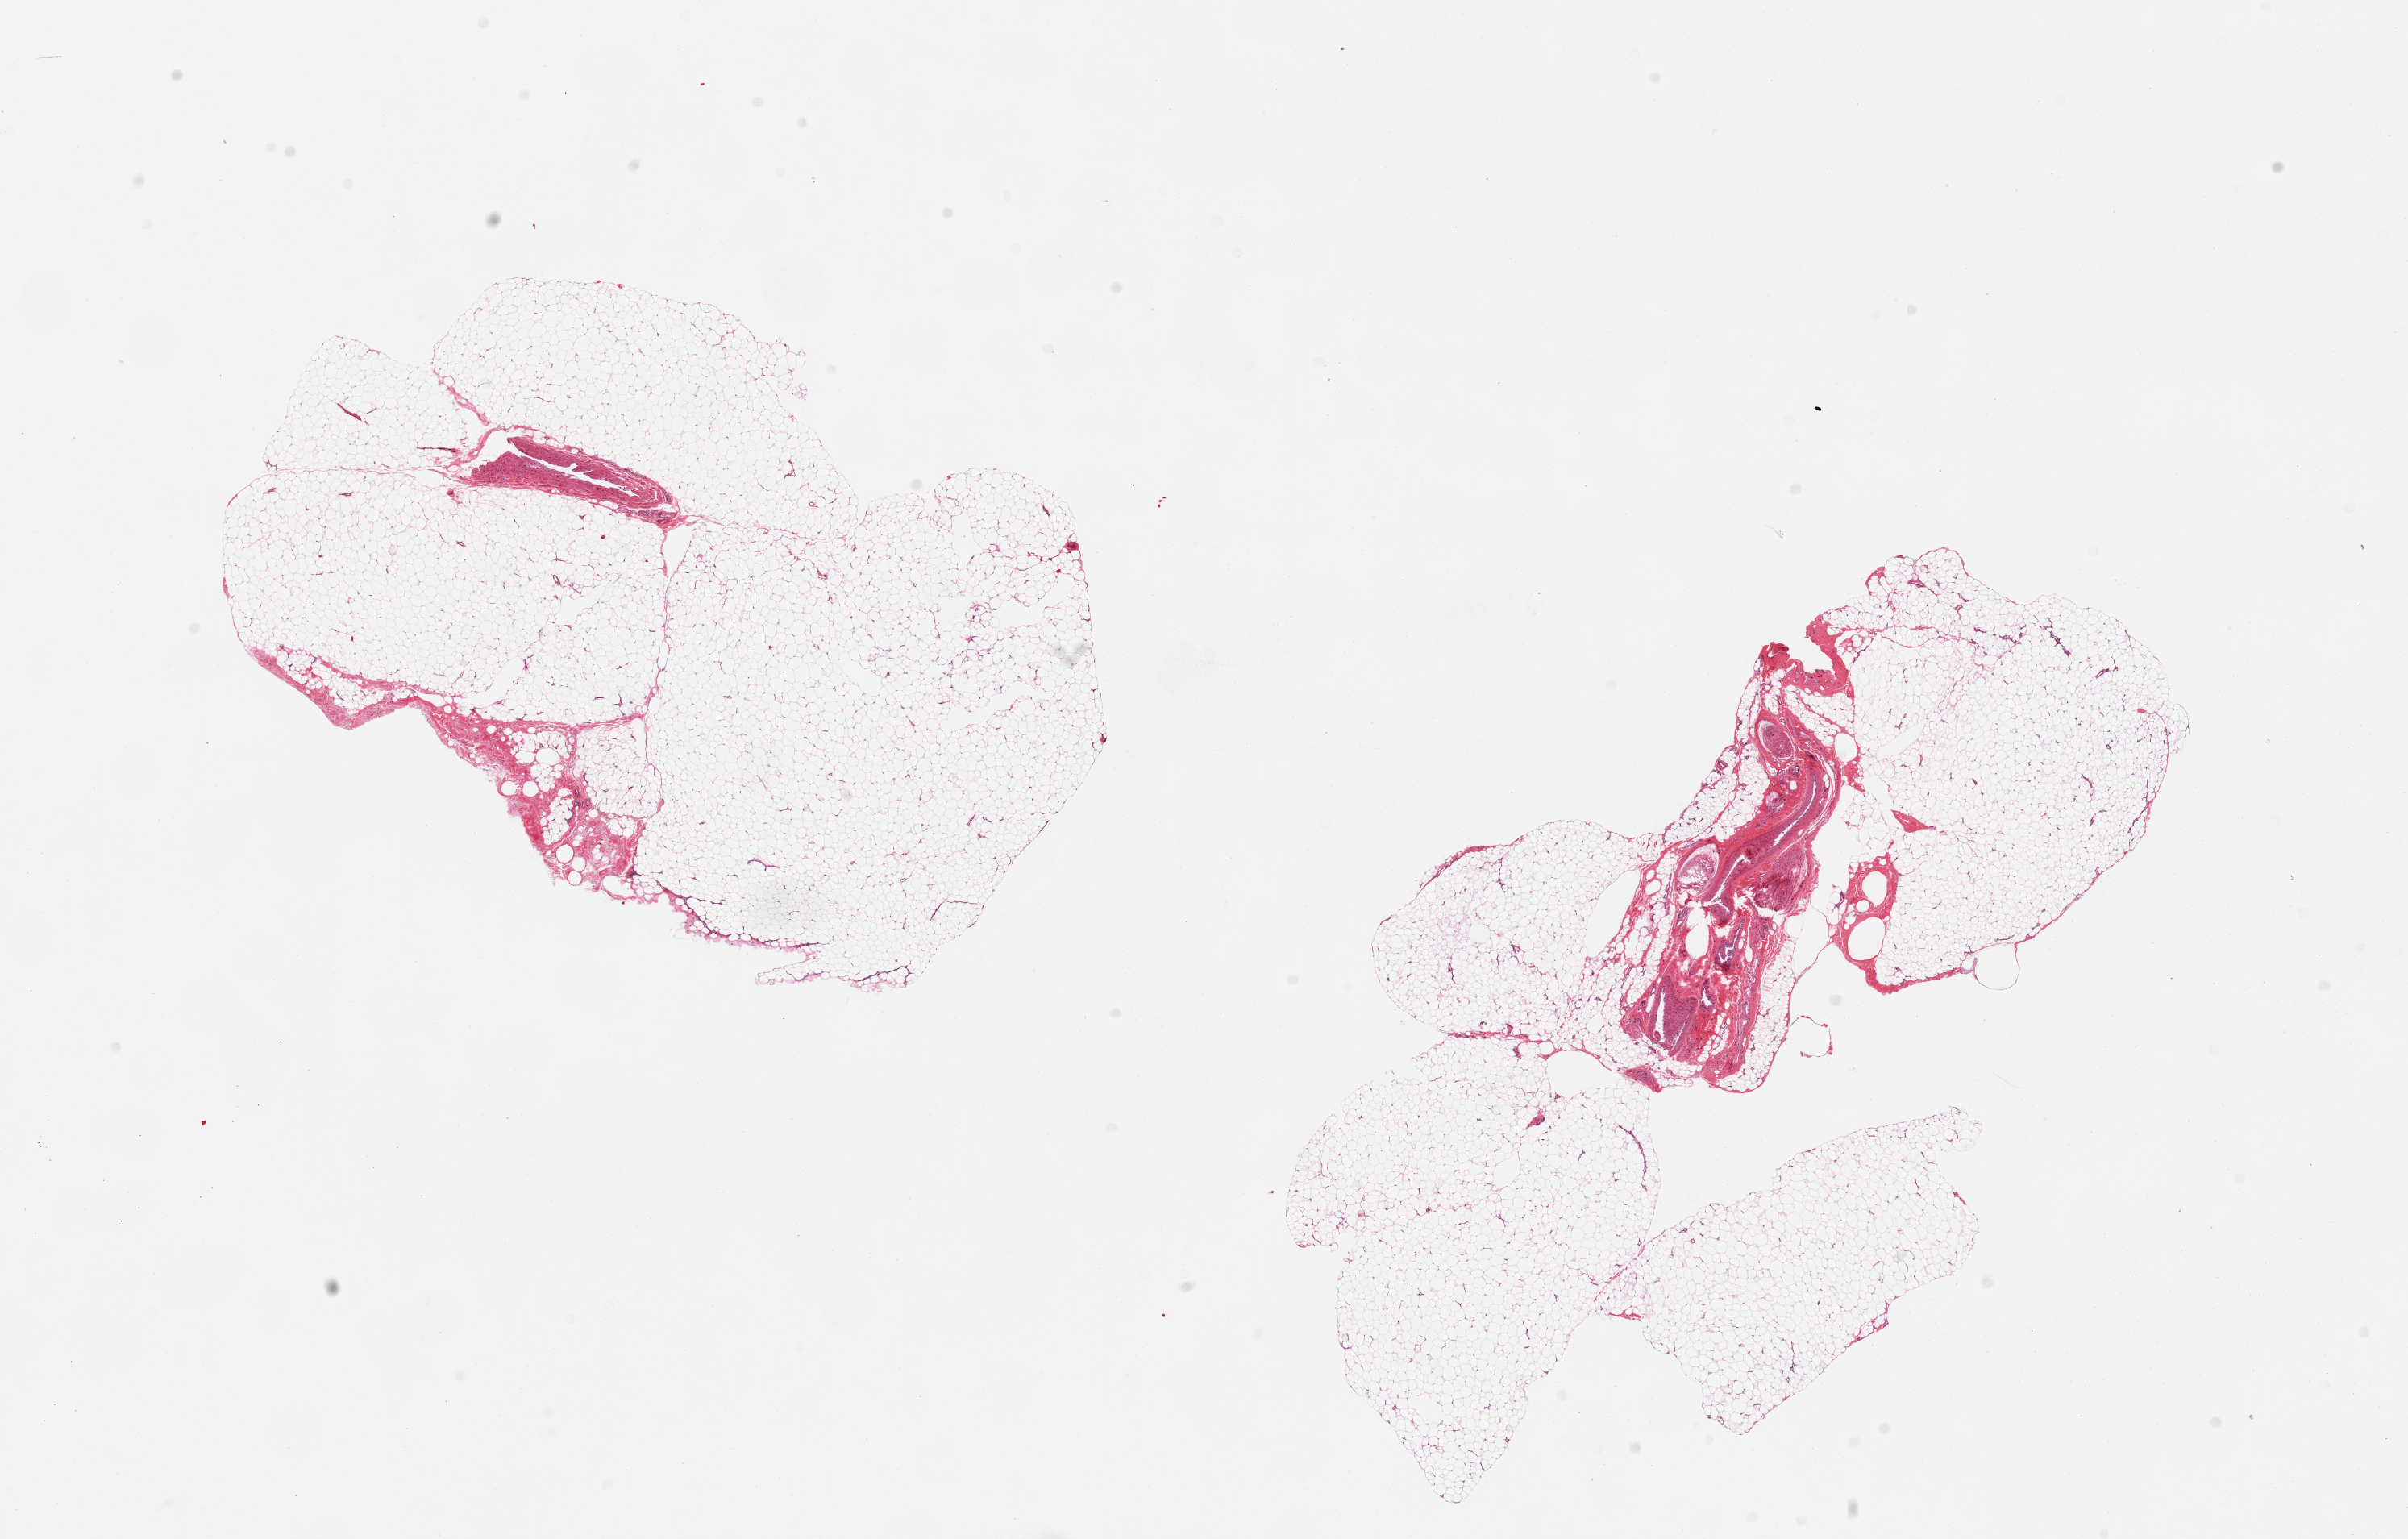
Whole-slide image, hematoxylin and eosin (H&E) stain, brightfield, a low-resolution overview of the entire scanned area, about 23.6 x 15.1 mm (from a 20x scan). PAXgene-fixed, paraffin-embedded tissue. Section of adipose tissue (target tissue). Donor tissue sample. Male donor.
Review note (as recorded): 2 pieces, one is ~20% nerve and vessels.